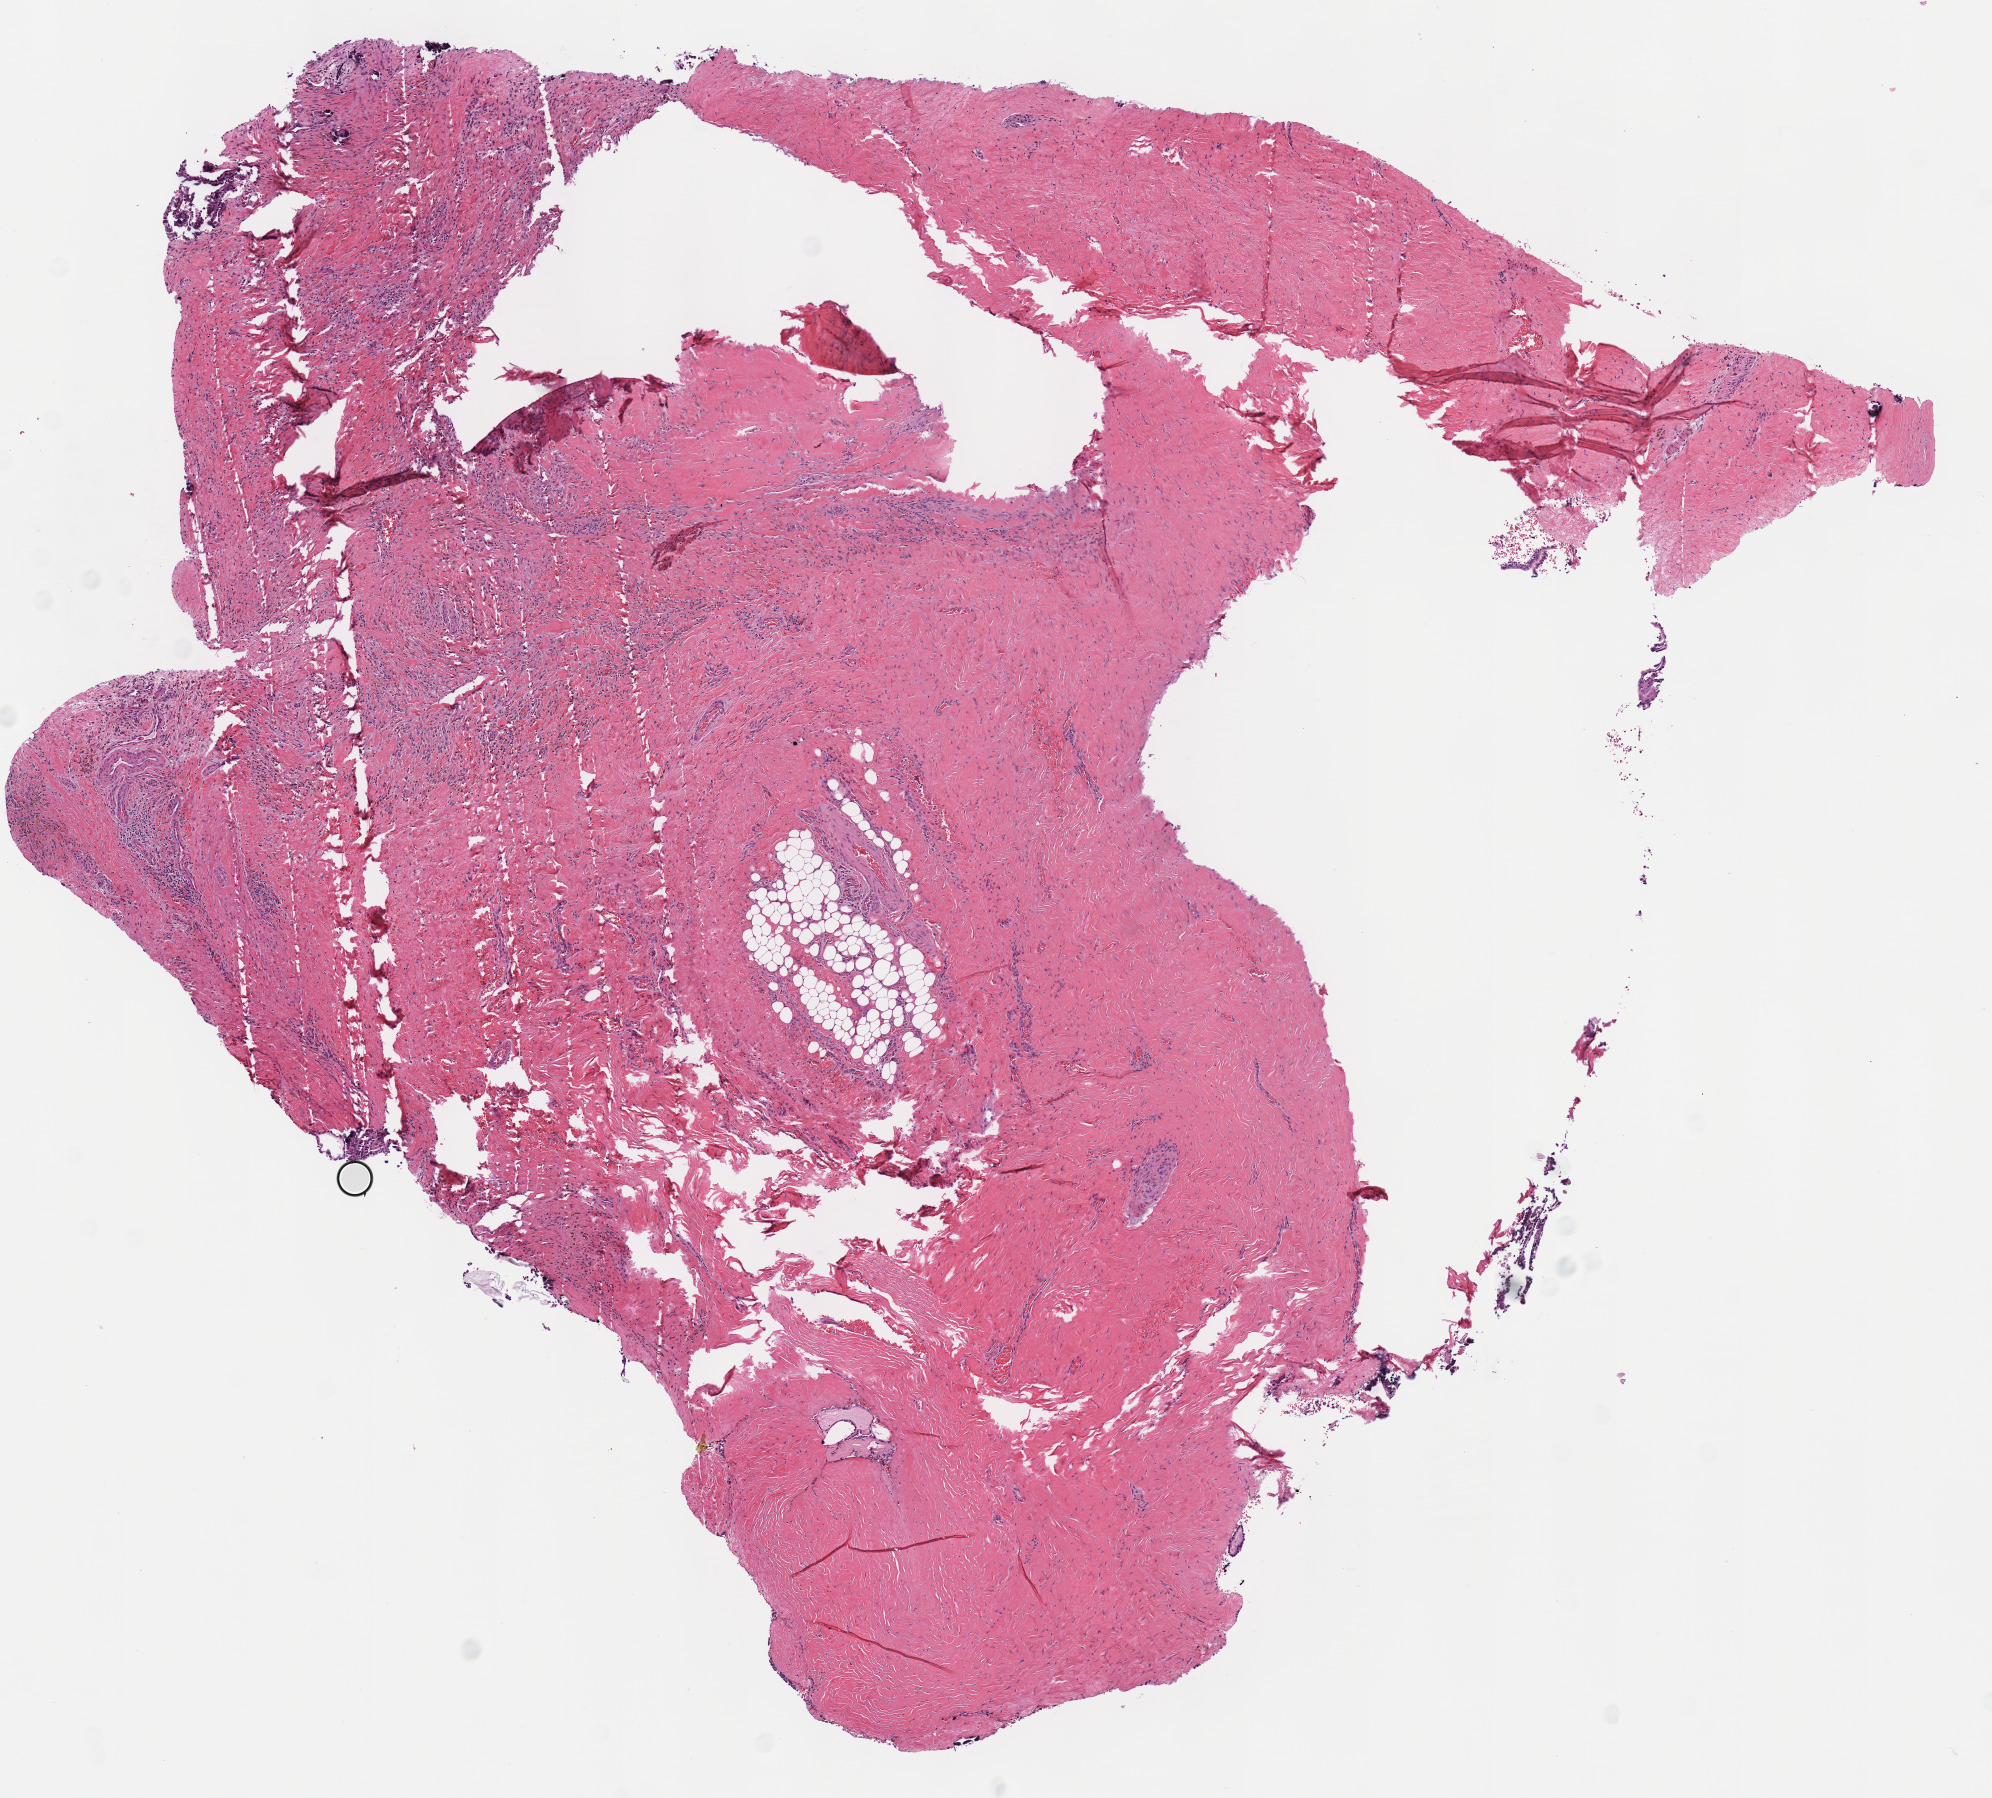
Digitized H&E tissue section (whole slide), low-resolution overview of the scanned area, about 7.8 x 7.1 mm; FFPE section; sample: primary tumour, thyroid. Male patient; age at initial diagnosis 51 years.
TNM: T3 N1a MX. Lymph nodes positive (case pathology): 4 of 4 examined. Histologic diagnosis: Papillary adenocarcinoma, NOS (thyroid gland). Laterality: midline. AJCC pathologic stage: III (7th edition).